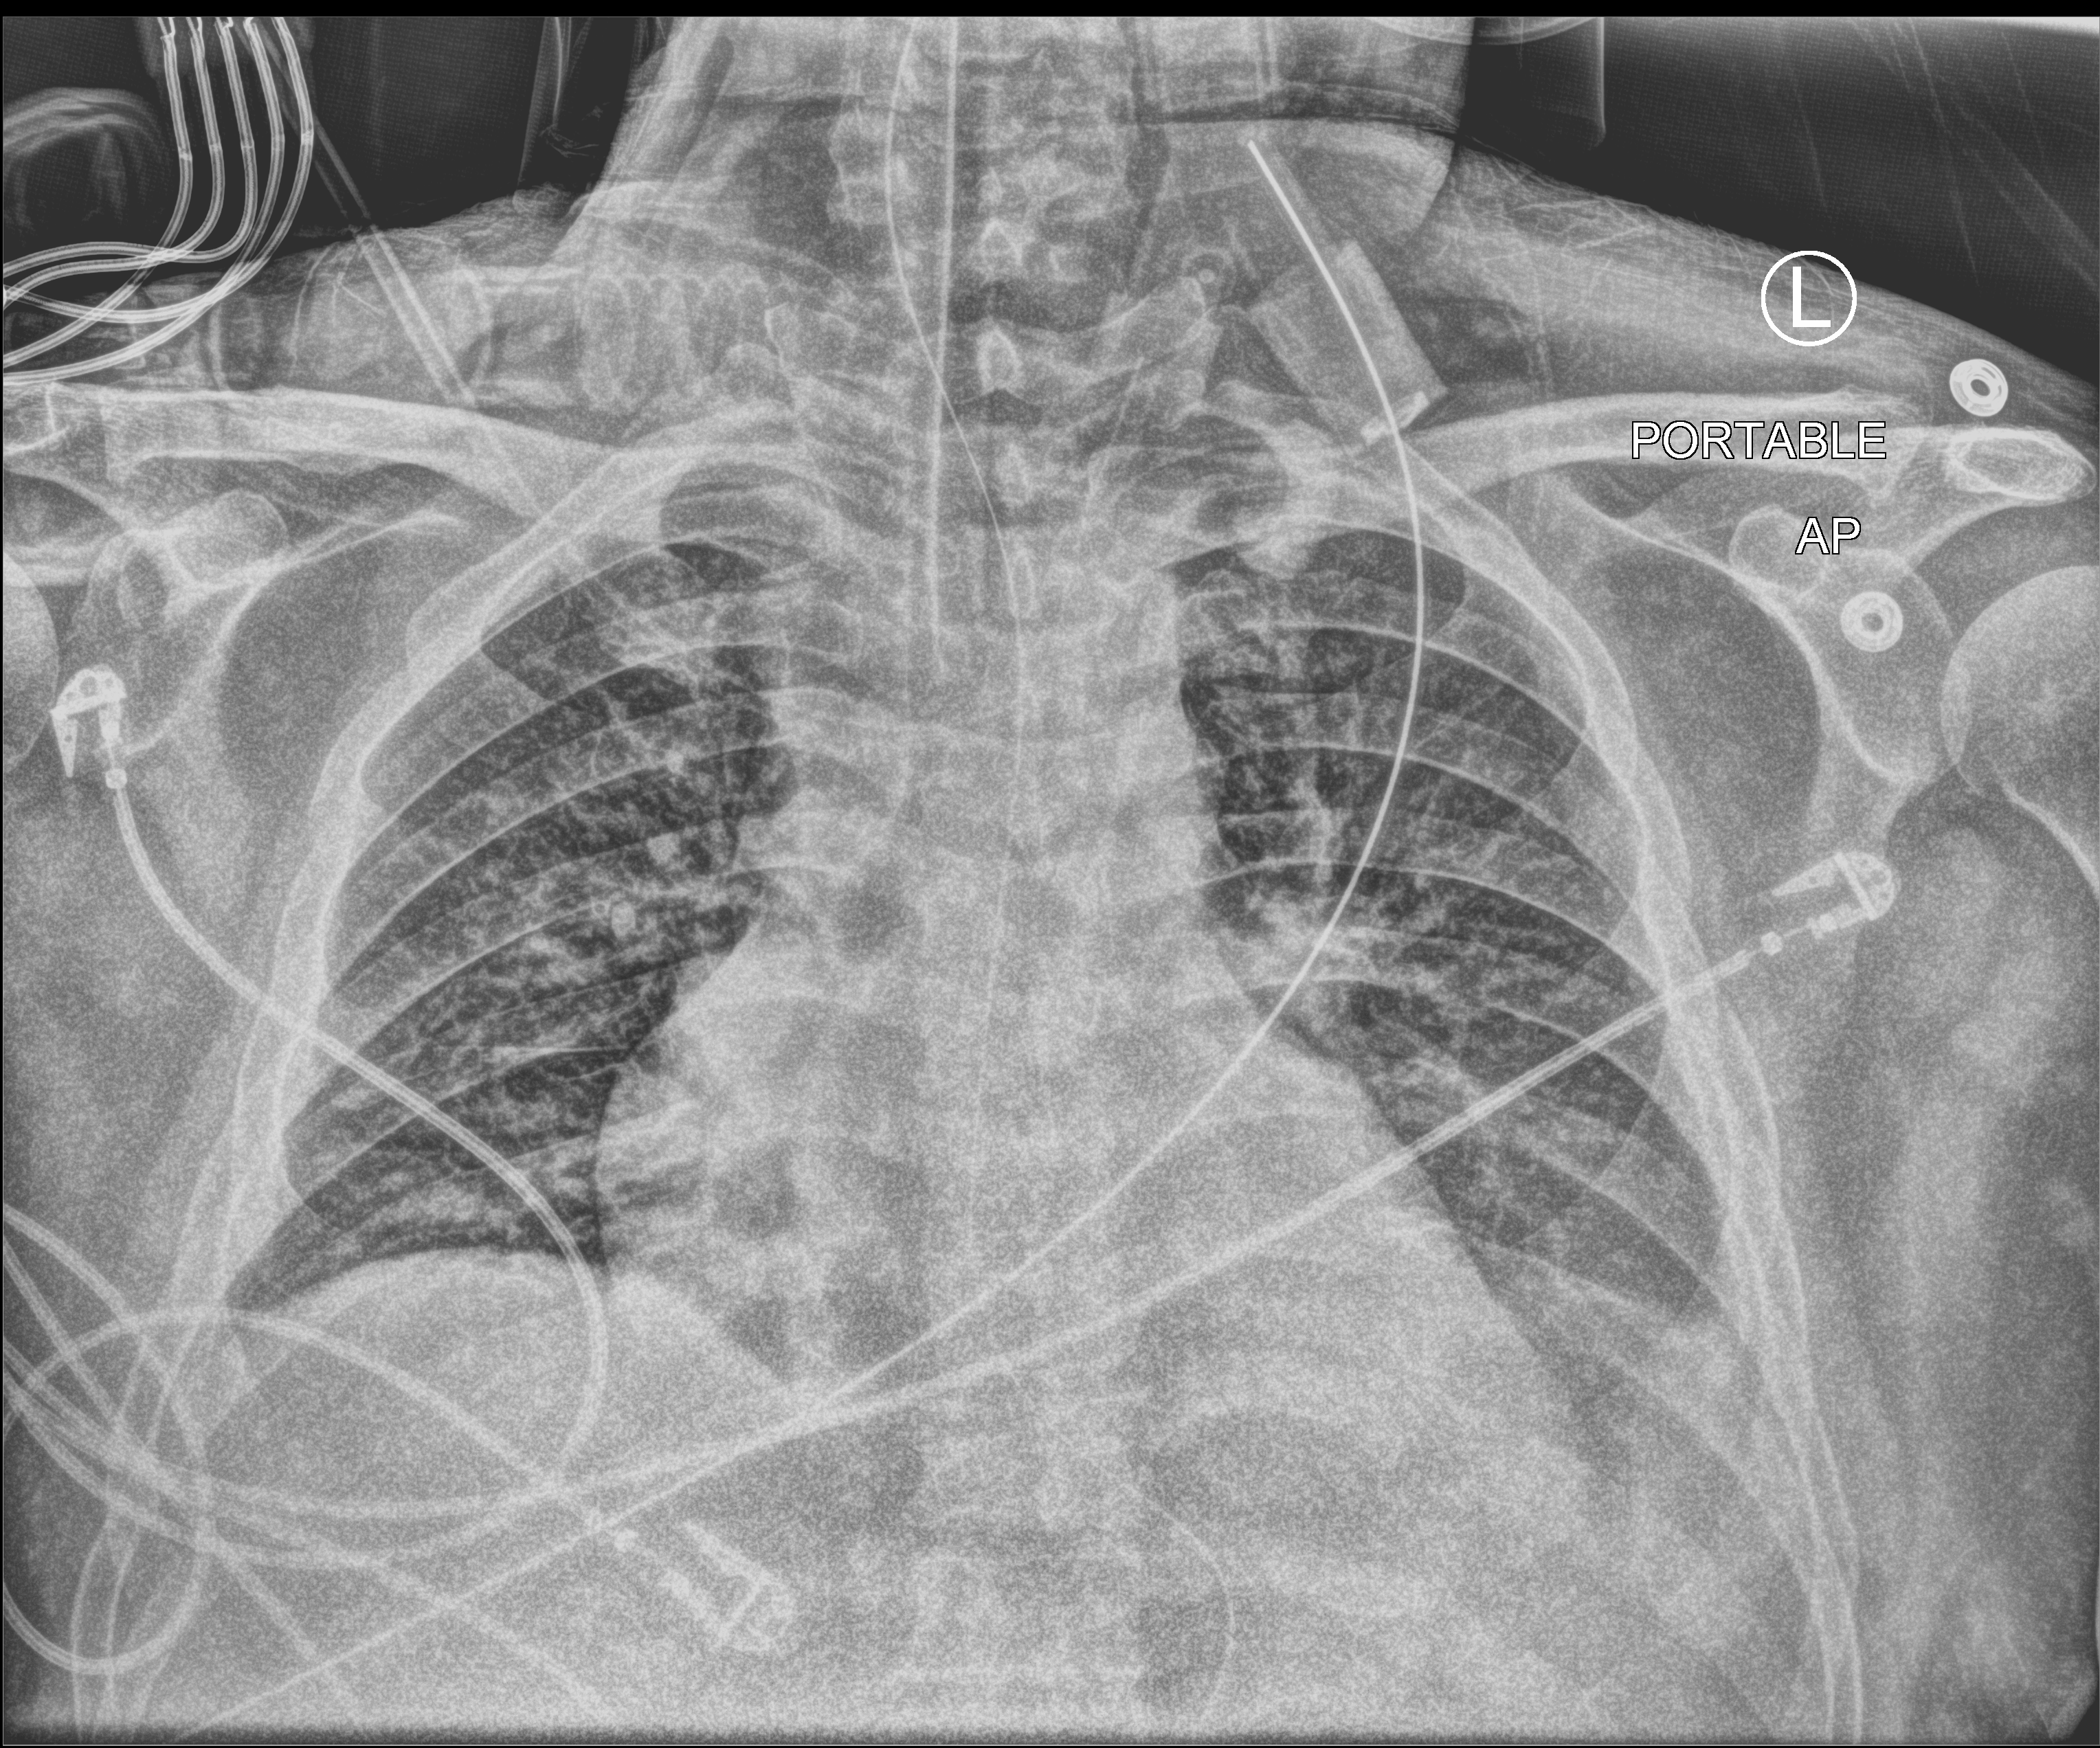
Bedside chest radiograph (computed radiography); anteroposterior (AP) projection. Male patient hospitalised with COVID-19, age 18–59 years.
Hospital-stay facts (about this admission, not read from this image; timing relative to this image not recorded): length of hospital stay: 65 days; admitted to intensive care during this hospital stay: yes.